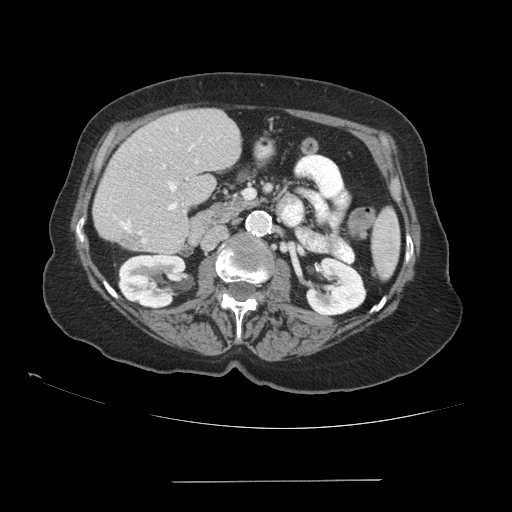
Contrast-enhanced abdominal CT (liver protocol), one axial slice. Position 39 of 89 along the scan axis. Reconstruction kernel STANDARD. 140 kVp. Soft-tissue window (W 400 / L 40 HU). 2.5 mm slice thickness. 512 × 512 image matrix. Case-level facts recorded for this patient, not image findings: diagnosis: hepatocellular carcinoma (patient treated with transarterial chemoembolisation; whether this scan precedes or follows treatment is not stated here); TNM stage (as recorded): Stage-IVA; Child-Pugh class: A; tumour differentiation: poorly differentiated; tumour nodularity: uninodular.
Outlined on this slice (semi-automatic segmentation, software-assisted and operator-edited):
- liver parenchyma outside the tumour (the mass and vessels are separate outlines, so this box may not span the whole liver): bounding box <92,108,240,252> (left, top, right, bottom; pixels)
- liver vessels: <114,128,197,243>